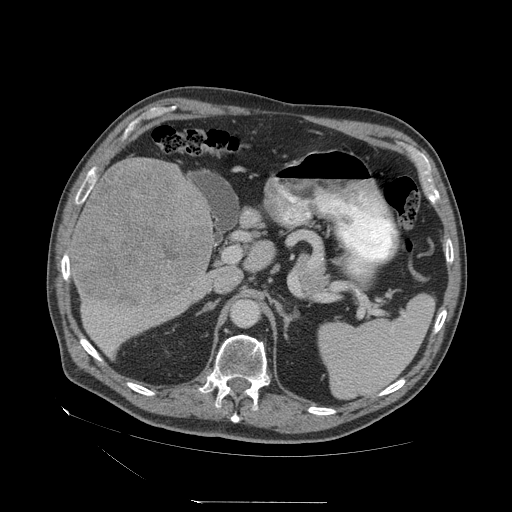
Contrast-enhanced abdominal CT (liver protocol), one axial slice. Position 28 of 83 along the scan axis. Reconstruction kernel STANDARD. Soft-tissue window (W 400 / L 40 HU). 512 × 512 image matrix, field of view 460 × 460 mm. From the clinical record (not read from this slice): diagnosis: hepatocellular carcinoma (patient treated with transarterial chemoembolisation; whether this scan precedes or follows treatment is not stated here); TNM stage (as recorded): Stage-I; Child-Pugh class: A; tumour differentiation: well differentiated; tumour nodularity: uninodular.
Annotated regions visible in this slice (semi-automatically segmented with operator editing):
- liver parenchyma outside the tumour (the mass and vessels are separate outlines, so this box may not span the whole liver): bounding box <68,158,215,358> (left, top, right, bottom; pixels)
- mass: <71,157,212,305>